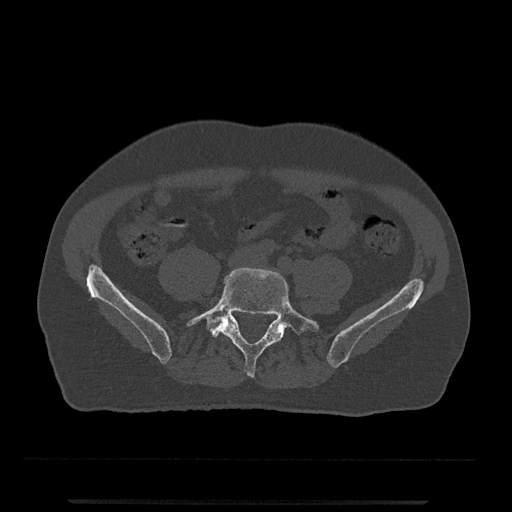
CT including the spine, one axial slice; slice 75 of 797 in the series (ordered by position); reconstruction kernel Br40s/3; bone window (W 1800 / L 400 HU); 0.5 mm slice thickness; 512 × 512 image matrix, field of view 419 × 419 mm. Male patient, age 63 years. Case-level facts recorded for this patient, not image findings: primary cancer: prostate.
Outlined on this slice (semi-automatically segmented with operator editing):
- L5 vertebra: bounding box [x1, y1, x2, y2] px = [186, 267, 320, 378]